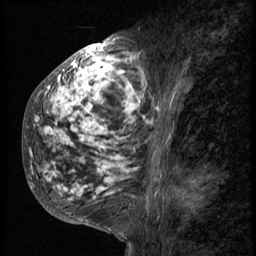
Breast MRI (dynamic contrast-enhanced), one sagittal slice; position 28 of 58 along the scan axis; 3 images stored at this slice position (order not interpretable as contrast timing); 1.5 T; TE 4.2 ms, TR 9 ms; 2.5 mm slice thickness; 256 × 256 image matrix, field of view 180 × 180 mm. Patient: female, 50 years. From the clinical record (not read from this slice): setting: breast cancer imaged before/during neoadjuvant chemotherapy; receptor status: triple-negative.
Outlined on this slice (semi-automatic segmentation, software-assisted and operator-edited):
- analysis volume of interest (the breast-tissue region the enhancement analysis was run in; not a lesion): bounding box [x1, y1, x2, y2] px = [23, 48, 156, 214]
- tumour enhancement mask (voxels above the 140 % enhancement threshold inside the analysis volume of interest): [30, 48, 156, 200]